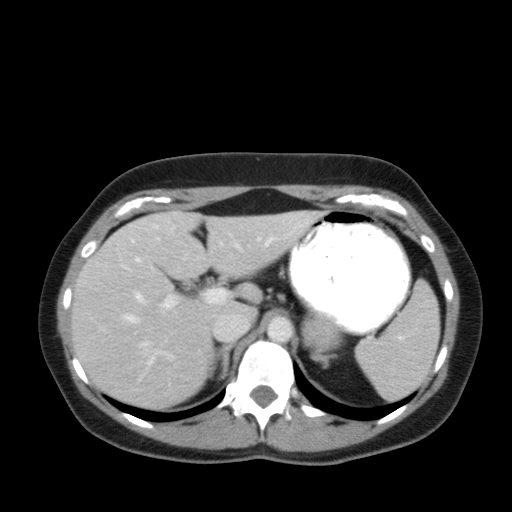
Contrast-enhanced abdominal CT, one axial slice; position 37 of 92 along the scan axis; reconstruction kernel FC12; 120 kVp; intravenous contrast given; soft-tissue window (W 400 / L 40 HU); 5 mm slice thickness; 512 × 512 image matrix. Female patient, age 35 years. Case-level facts recorded for this patient, not image findings: diagnosis: adrenocortical carcinoma; tumour side: left adrenal; tumour size at pathology: 6.6 cm; Ki-67 index: 5 %.
Annotated regions visible in this slice (semi-automatically segmented with operator editing):
- mass: bounding box [x1, y1, x2, y2] px = [303, 316, 340, 350]